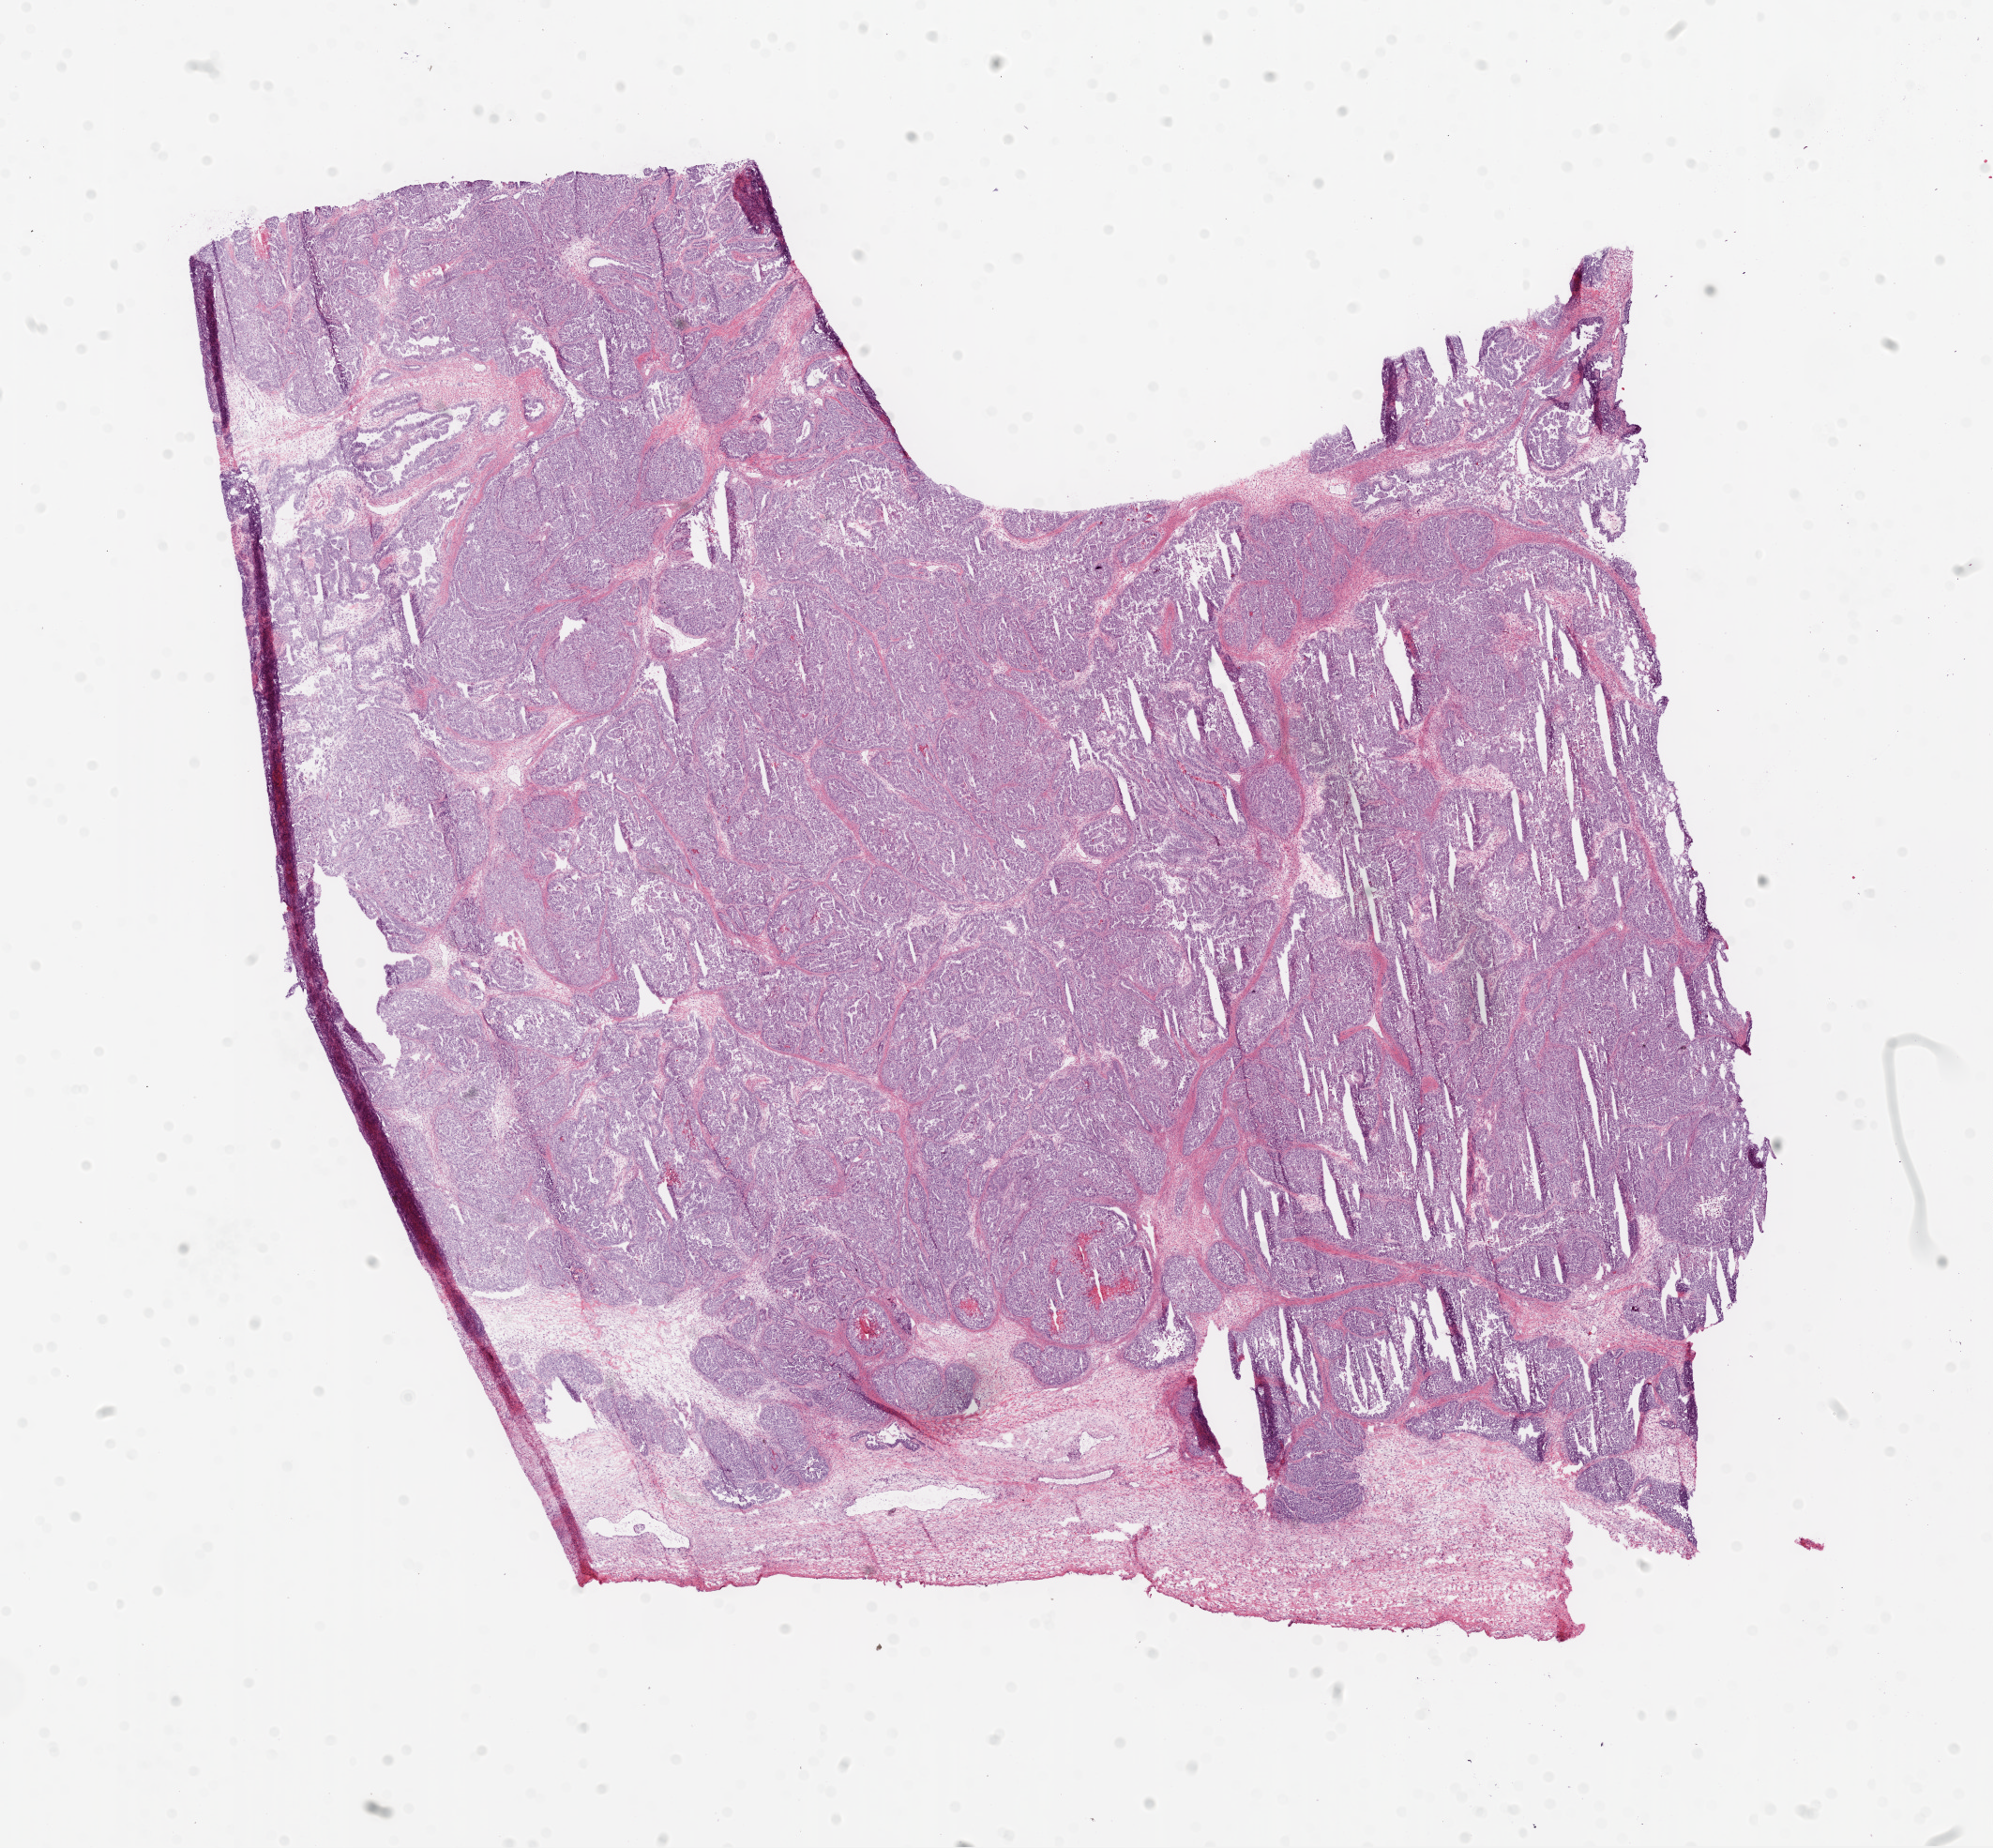
Digitized Hematoxylin and eosin (H&E) stained tissue section (whole slide), low-resolution overview of the scanned area, about 17.1 x 15.8 mm, frozen section from the bottom of the tissue portion, primary tumour sample from the ovary. Female patient; age at initial diagnosis 76 years. Histologic grade: G3 (poorly differentiated). Slide review estimates, as recorded: tumour cells 89%, tumour nuclei 90%, normal cells 0%, stromal cells 10%, necrosis 1%.
* laterality: bilateral
* histologic diagnosis: Serous cystadenocarcinoma, NOS
* FIGO stage: IIIC